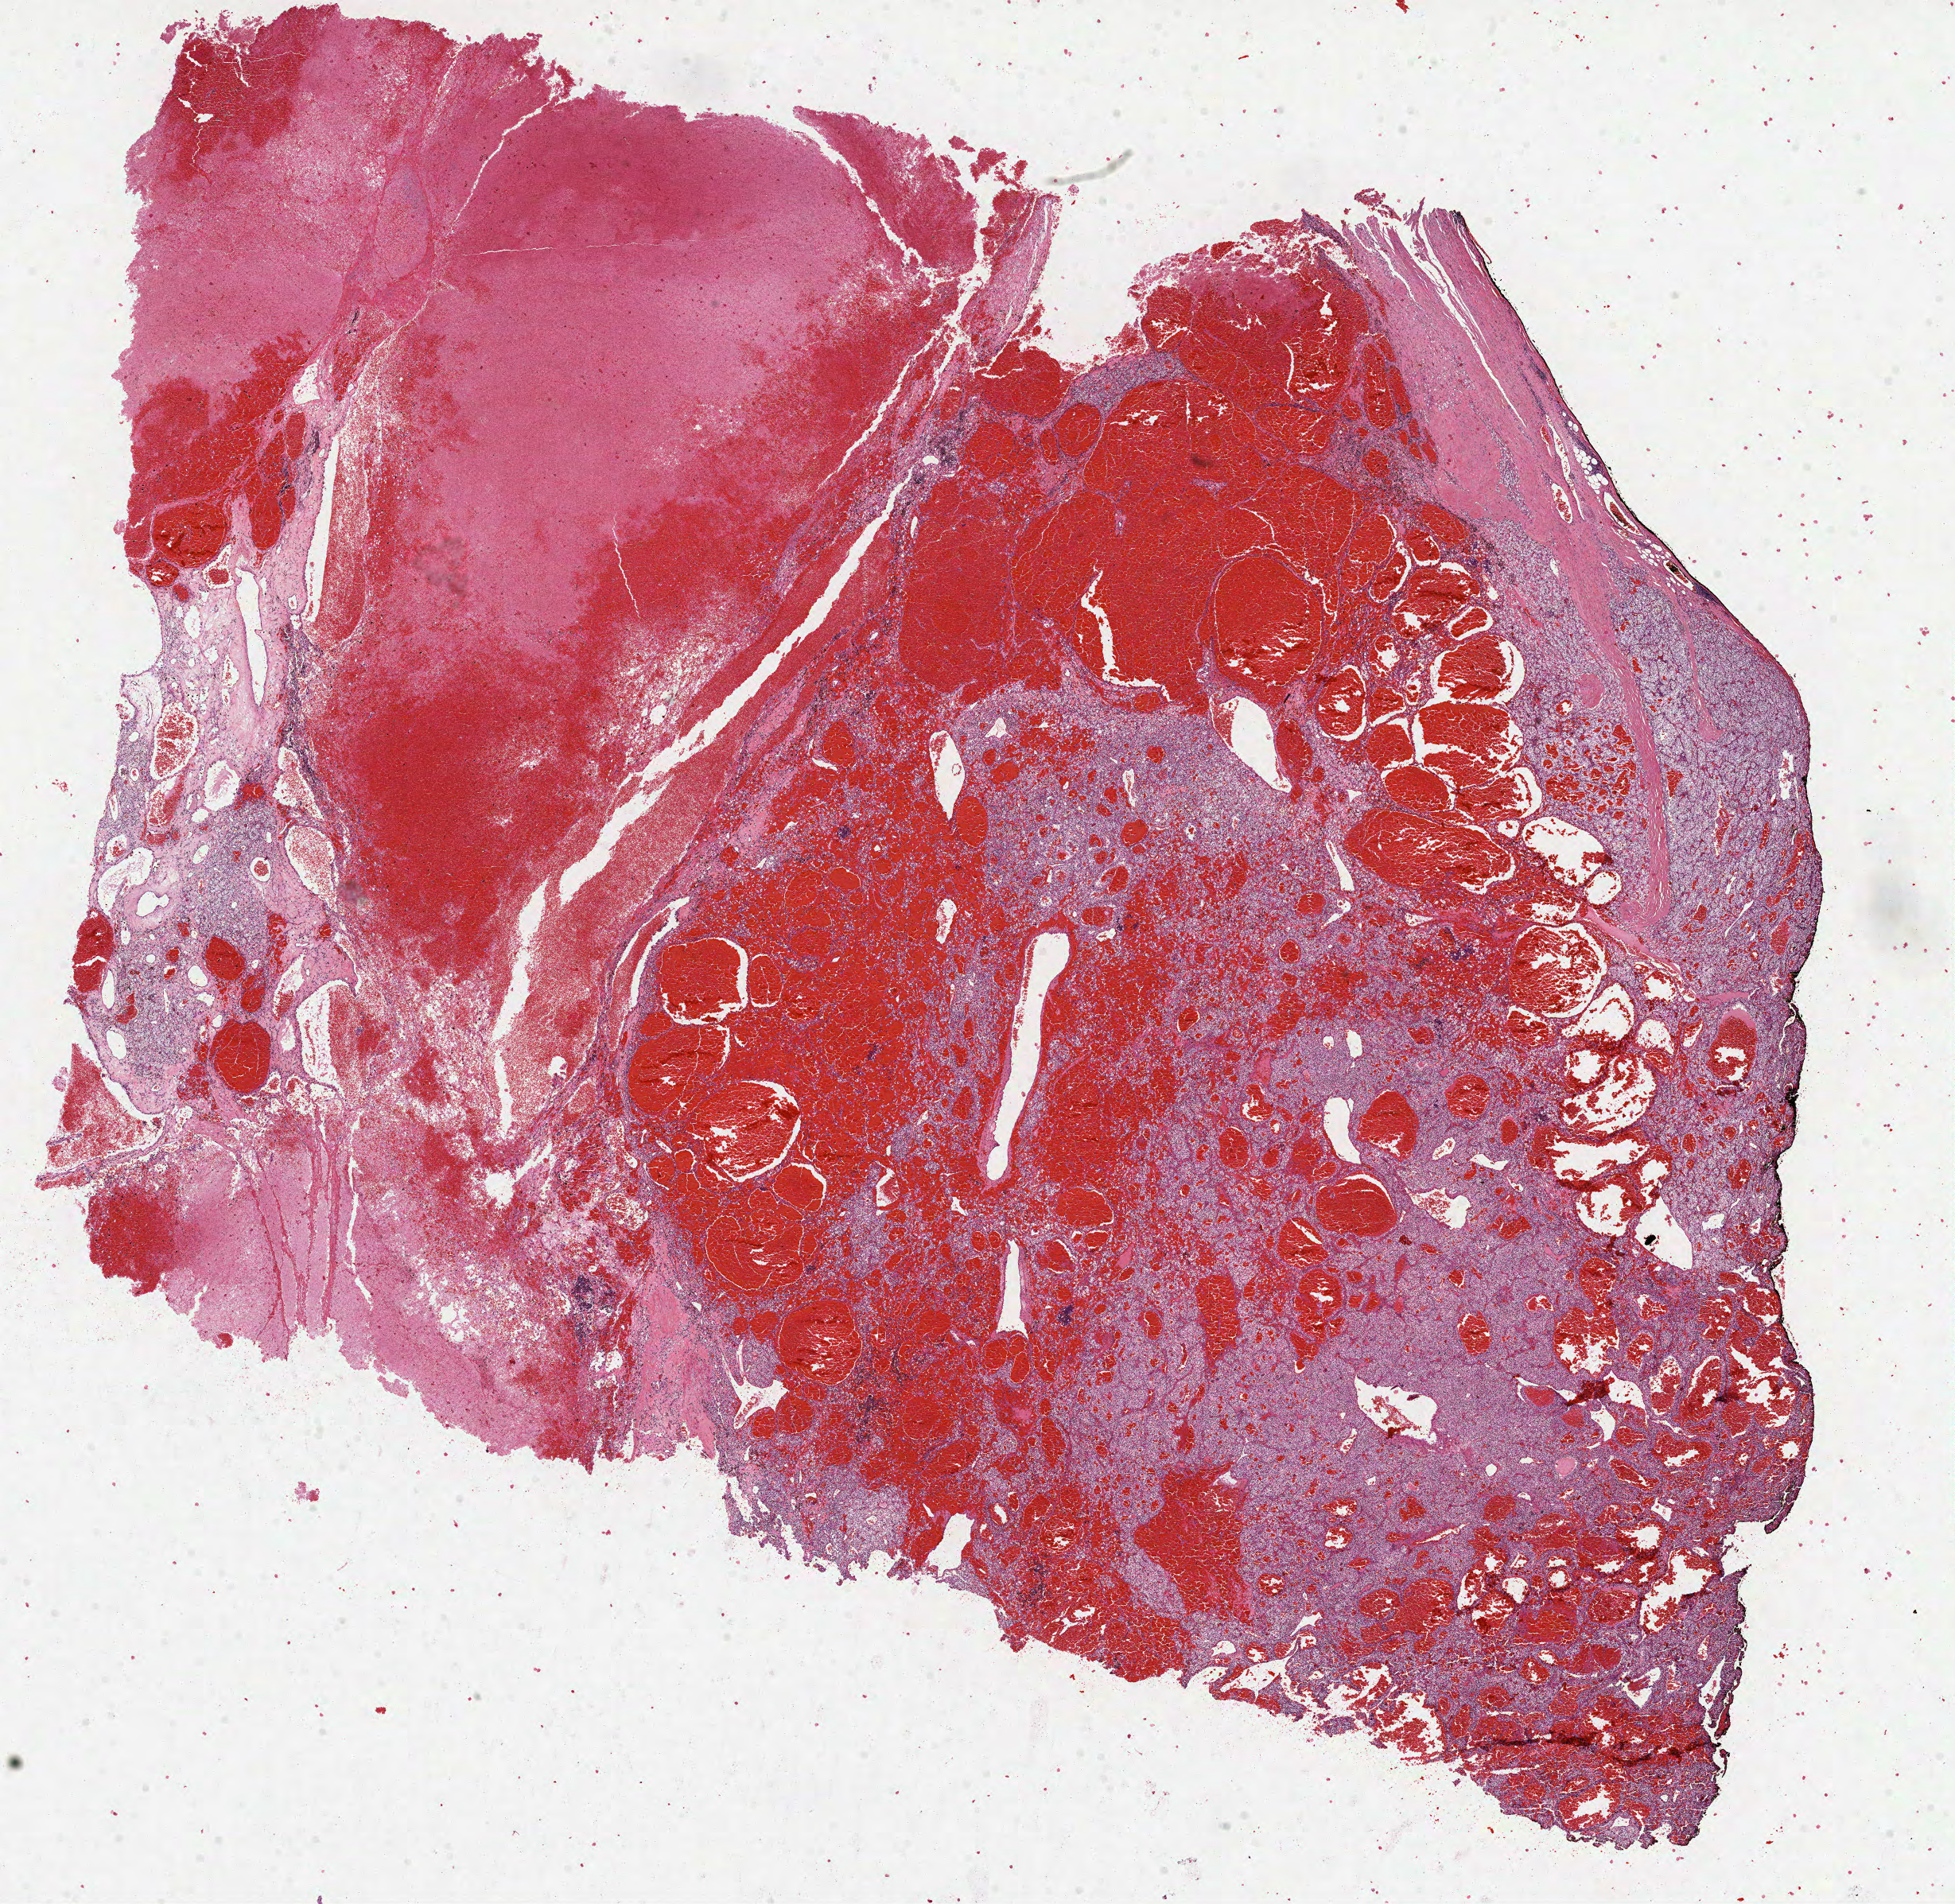
Digitized H&E-stained tissue section (whole slide), low-resolution overview of the scanned area, about 19.8 x 19.3 mm (from a 40x scan), formalin-fixed paraffin-embedded (FFPE) diagnostic section, primary tumour sample from the kidney. Female patient; age at initial diagnosis 75 years. Histologic grade: G3 (poorly differentiated).
Diagnosis: Clear cell adenocarcinoma, NOS. AJCC pathologic stage: III (7th edition).